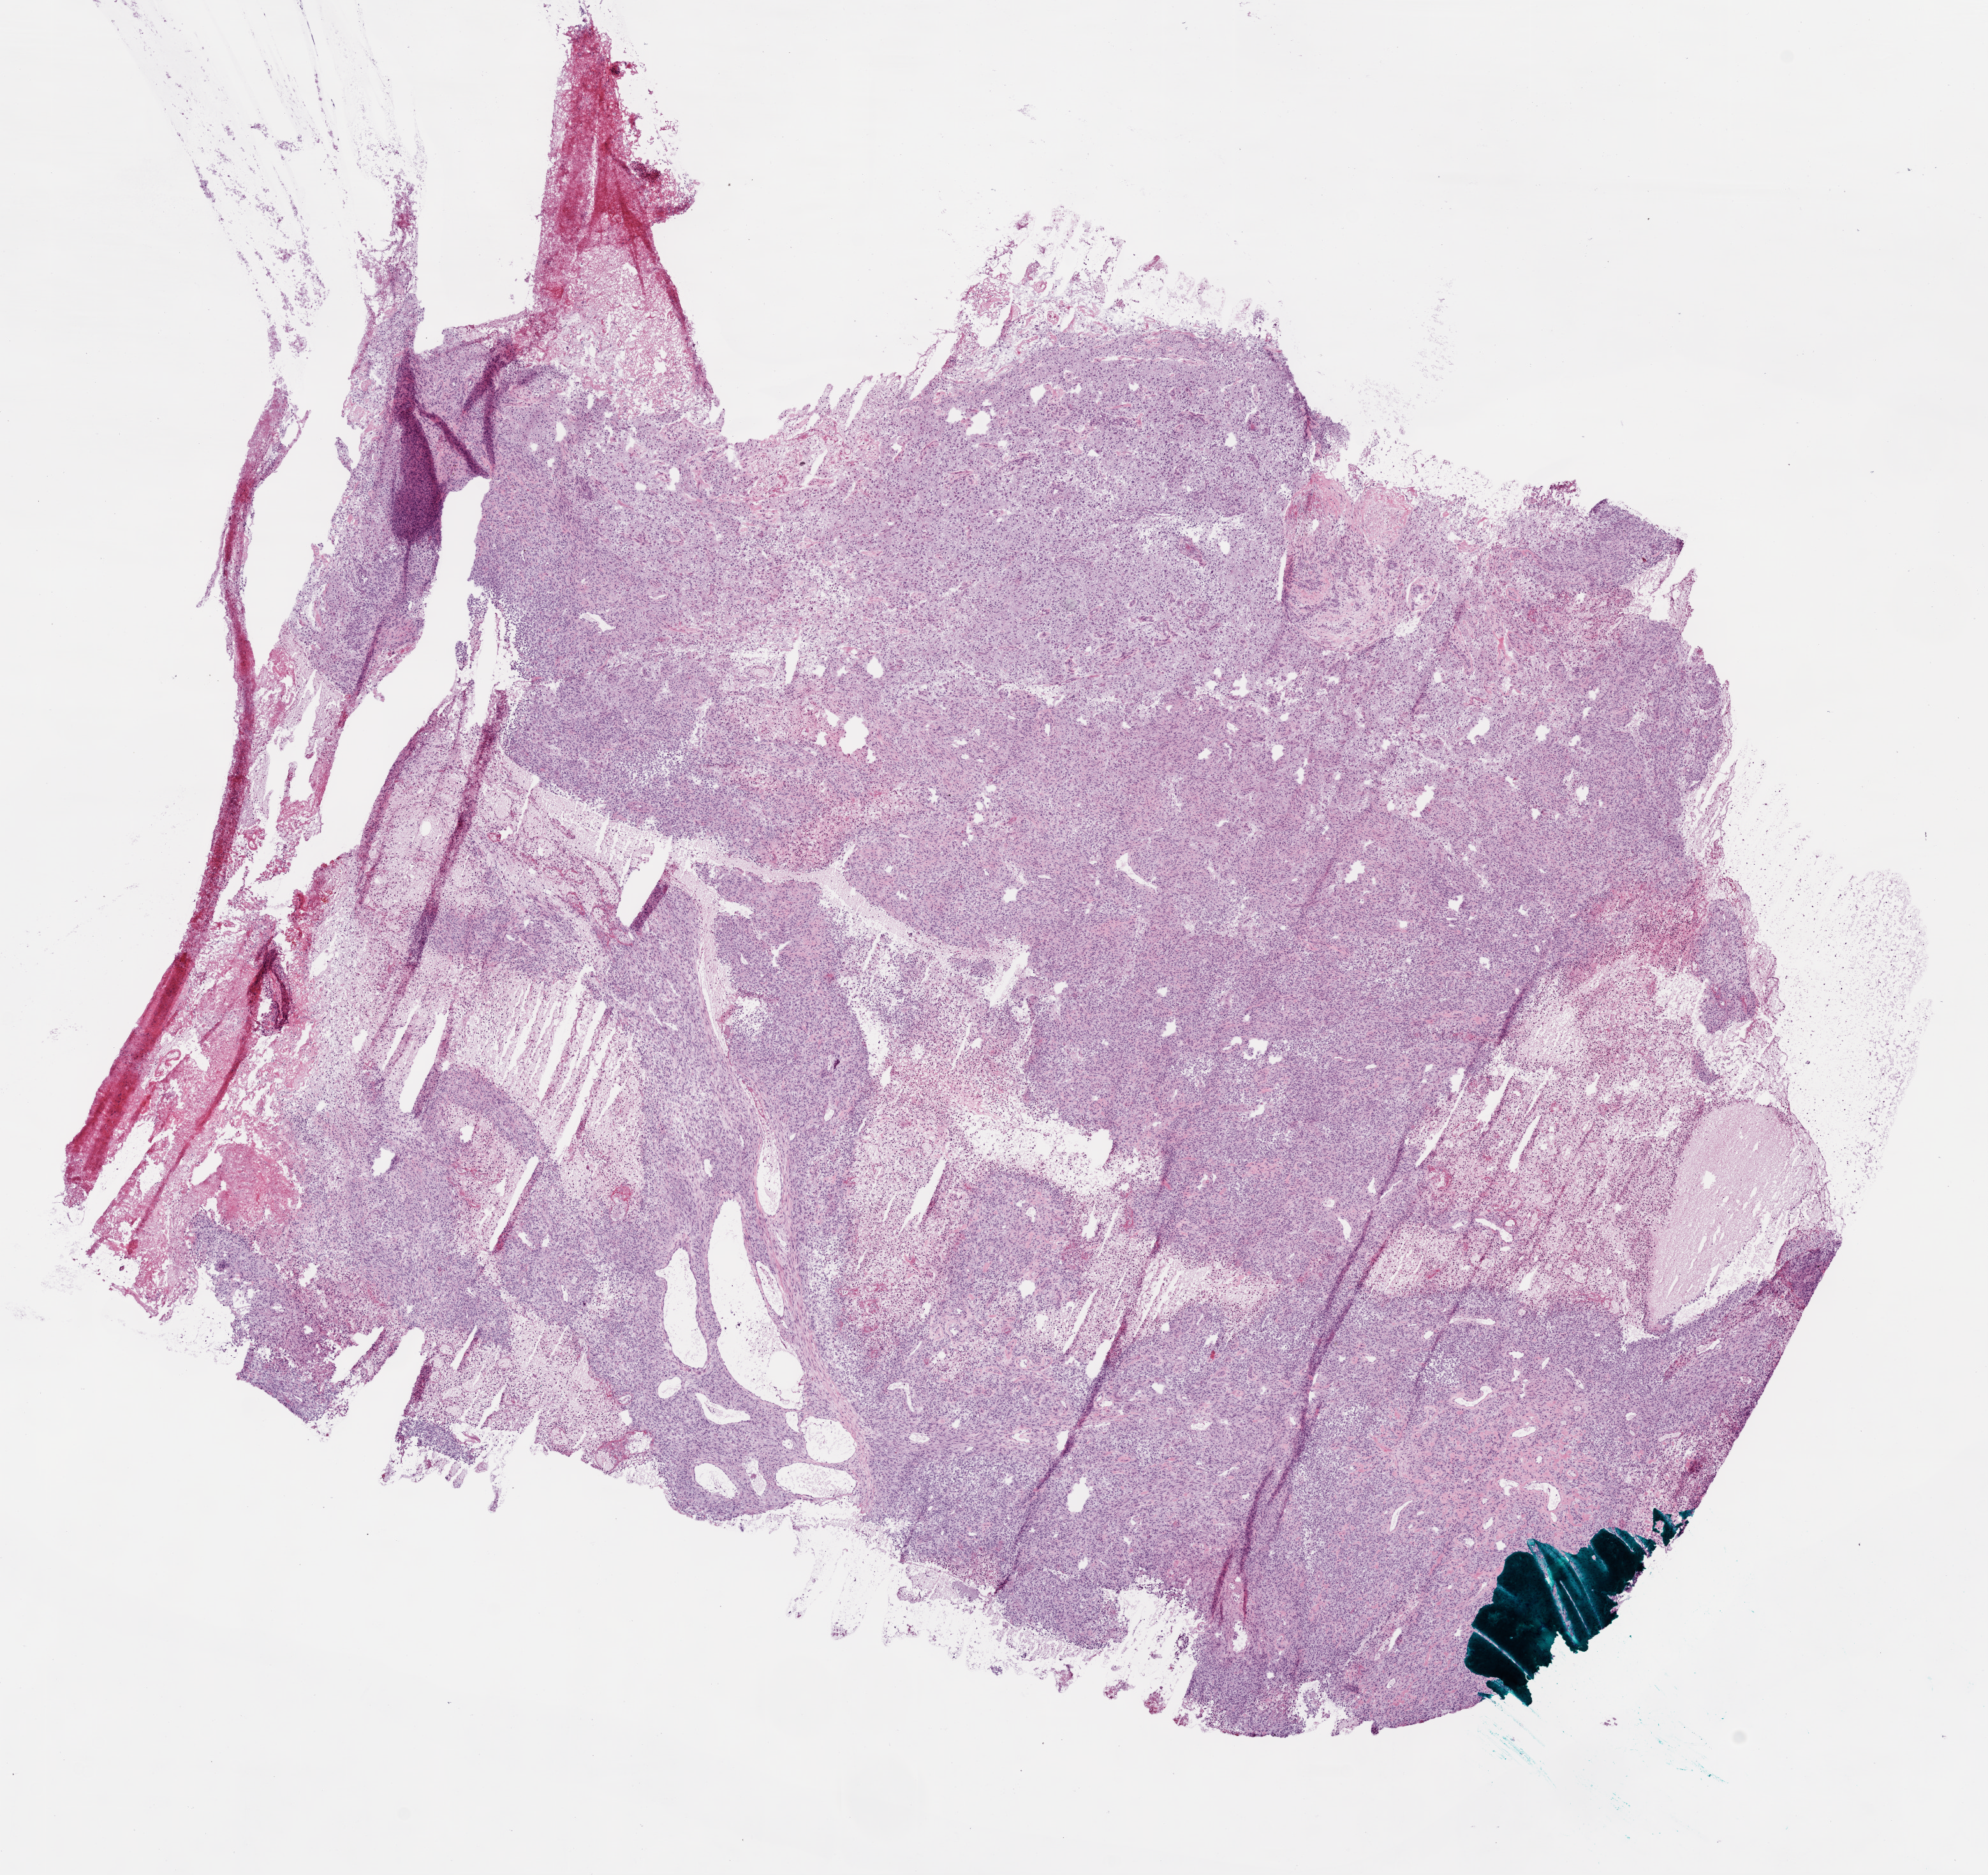
Whole-slide histology image, H&E — whole scanned area (about 12.6 x 11.9 mm) shown as a low-resolution overview. Frozen section from the bottom of the tissue portion. Primary tumour sample from the brain. Male patient; age at initial diagnosis 61 years. Pathologist review of this section (percent, as recorded): tumour cells 80%, tumour nuclei 90%, stromal cells 10%, necrosis 10%.
Pathologic diagnosis: Glioblastoma.